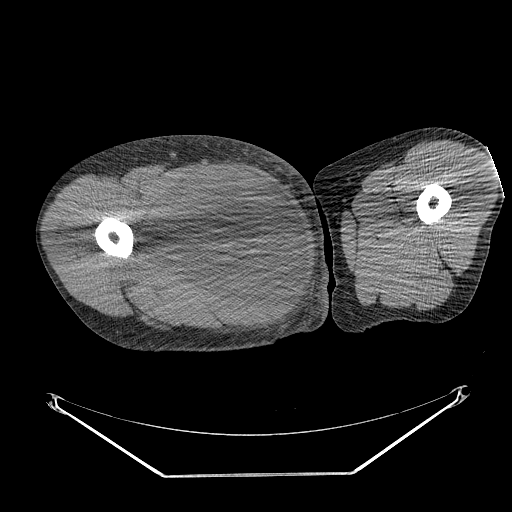
CT of an extremity soft-tissue mass (from a PET/CT study), one axial slice. Position 258 of 311 along the scan axis. 140 kVp. Soft-tissue window (W 400 / L 40 HU). 512 × 512 image matrix, field of view 500 × 500 mm. Male patient. From the clinical record (not read from this slice): histological type: undifferentiated - pleiomorphic; grade: high; site of the primary tumour: right thigh.
Annotated regions visible in this slice (expert contour drawn on MRI and transferred to this co-registered scan by the dataset authors):
- gross tumour volume including surrounding oedema: bounding box <141,169,266,277> (left, top, right, bottom; pixels)
- gross tumour volume (mass): <153,169,266,273>